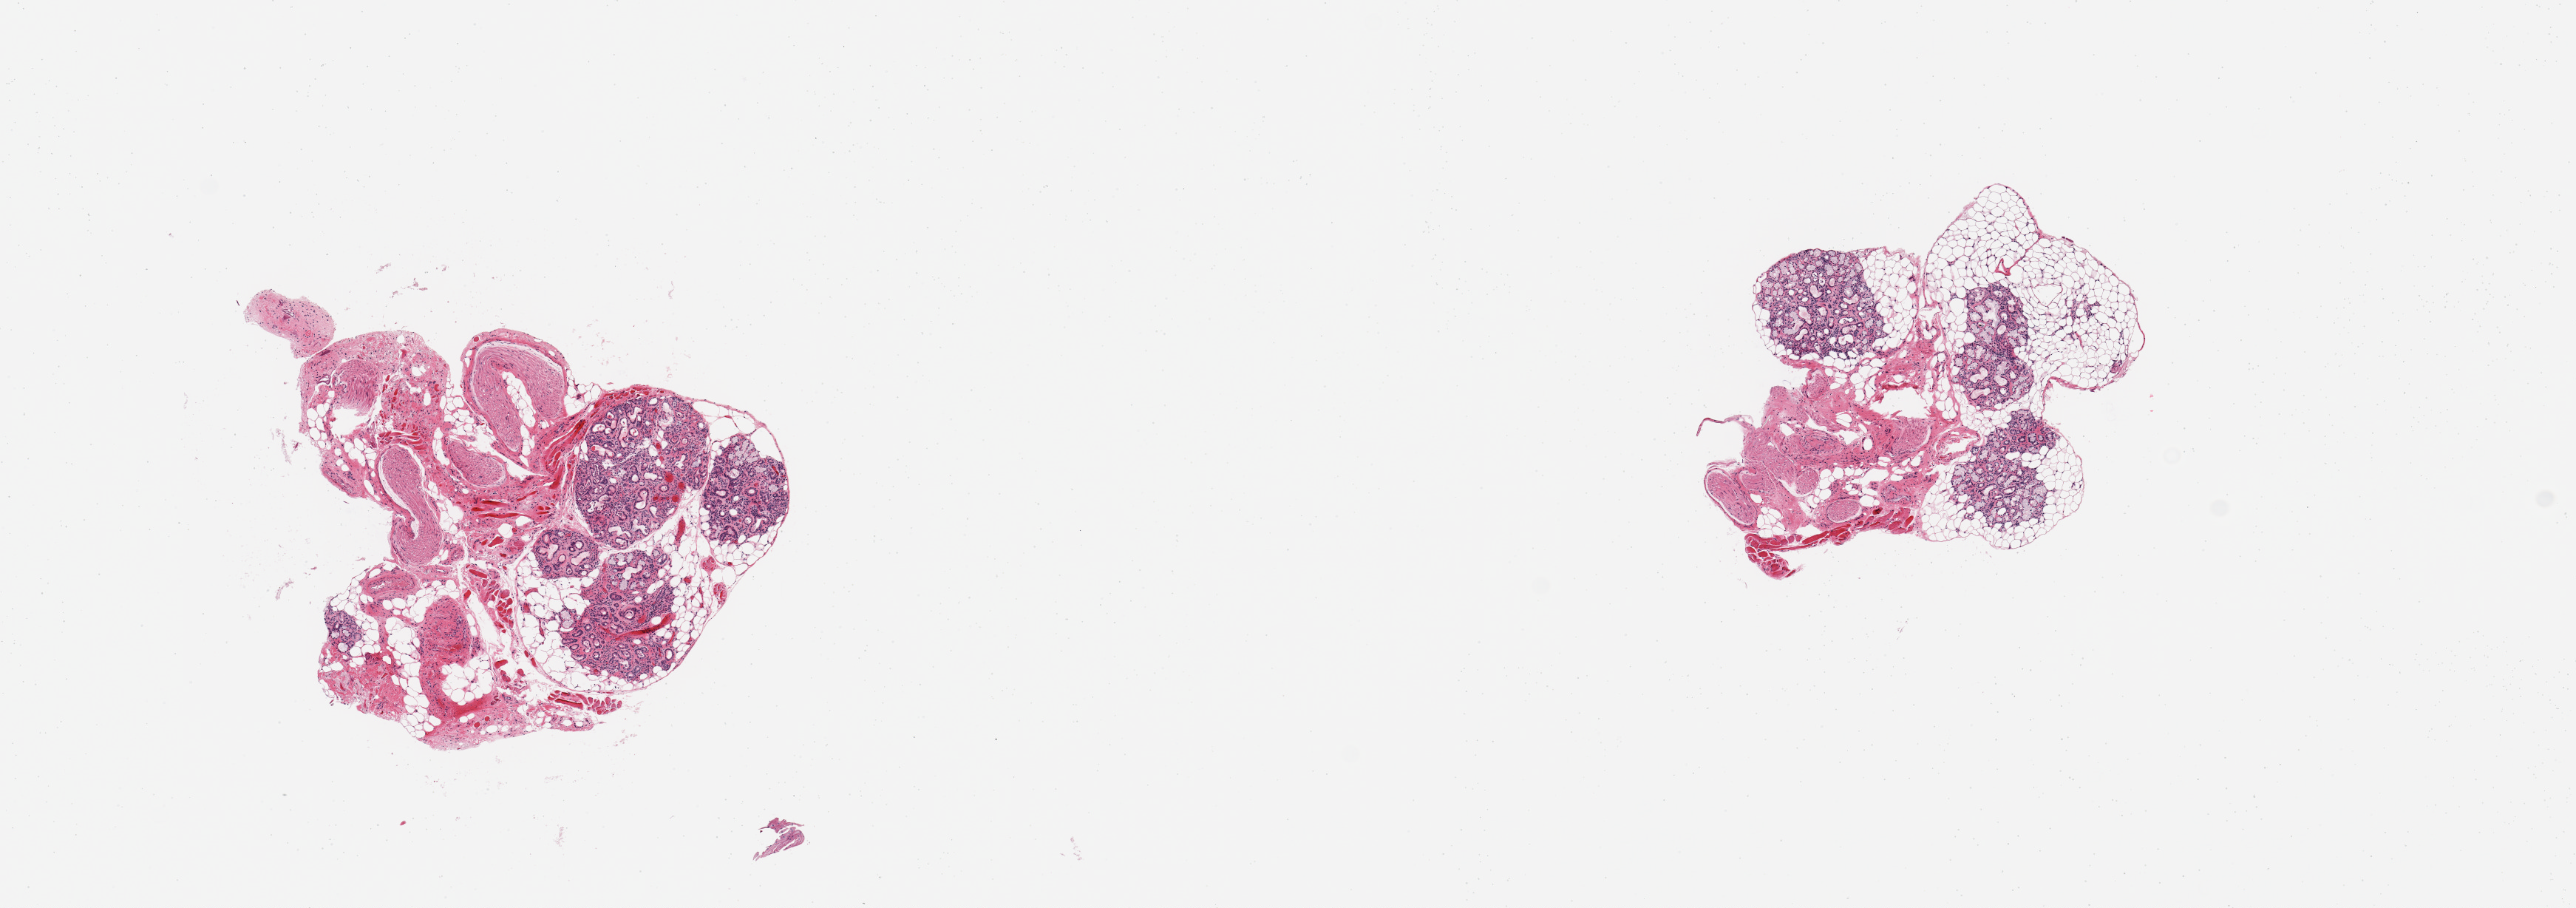
Whole-slide image, haematoxylin and eosin stain, whole scanned area (about 13.8 x 4.9 mm) shown as a low-resolution overview; PAXgene-fixed, paraffin-embedded tissue; sampled site (target tissue): minor salivary gland; donor tissue sample. Male donor.
• reviewer comment on this tissue sample: 2 pieces, ~30% glandular elements; rest is stroma/fat